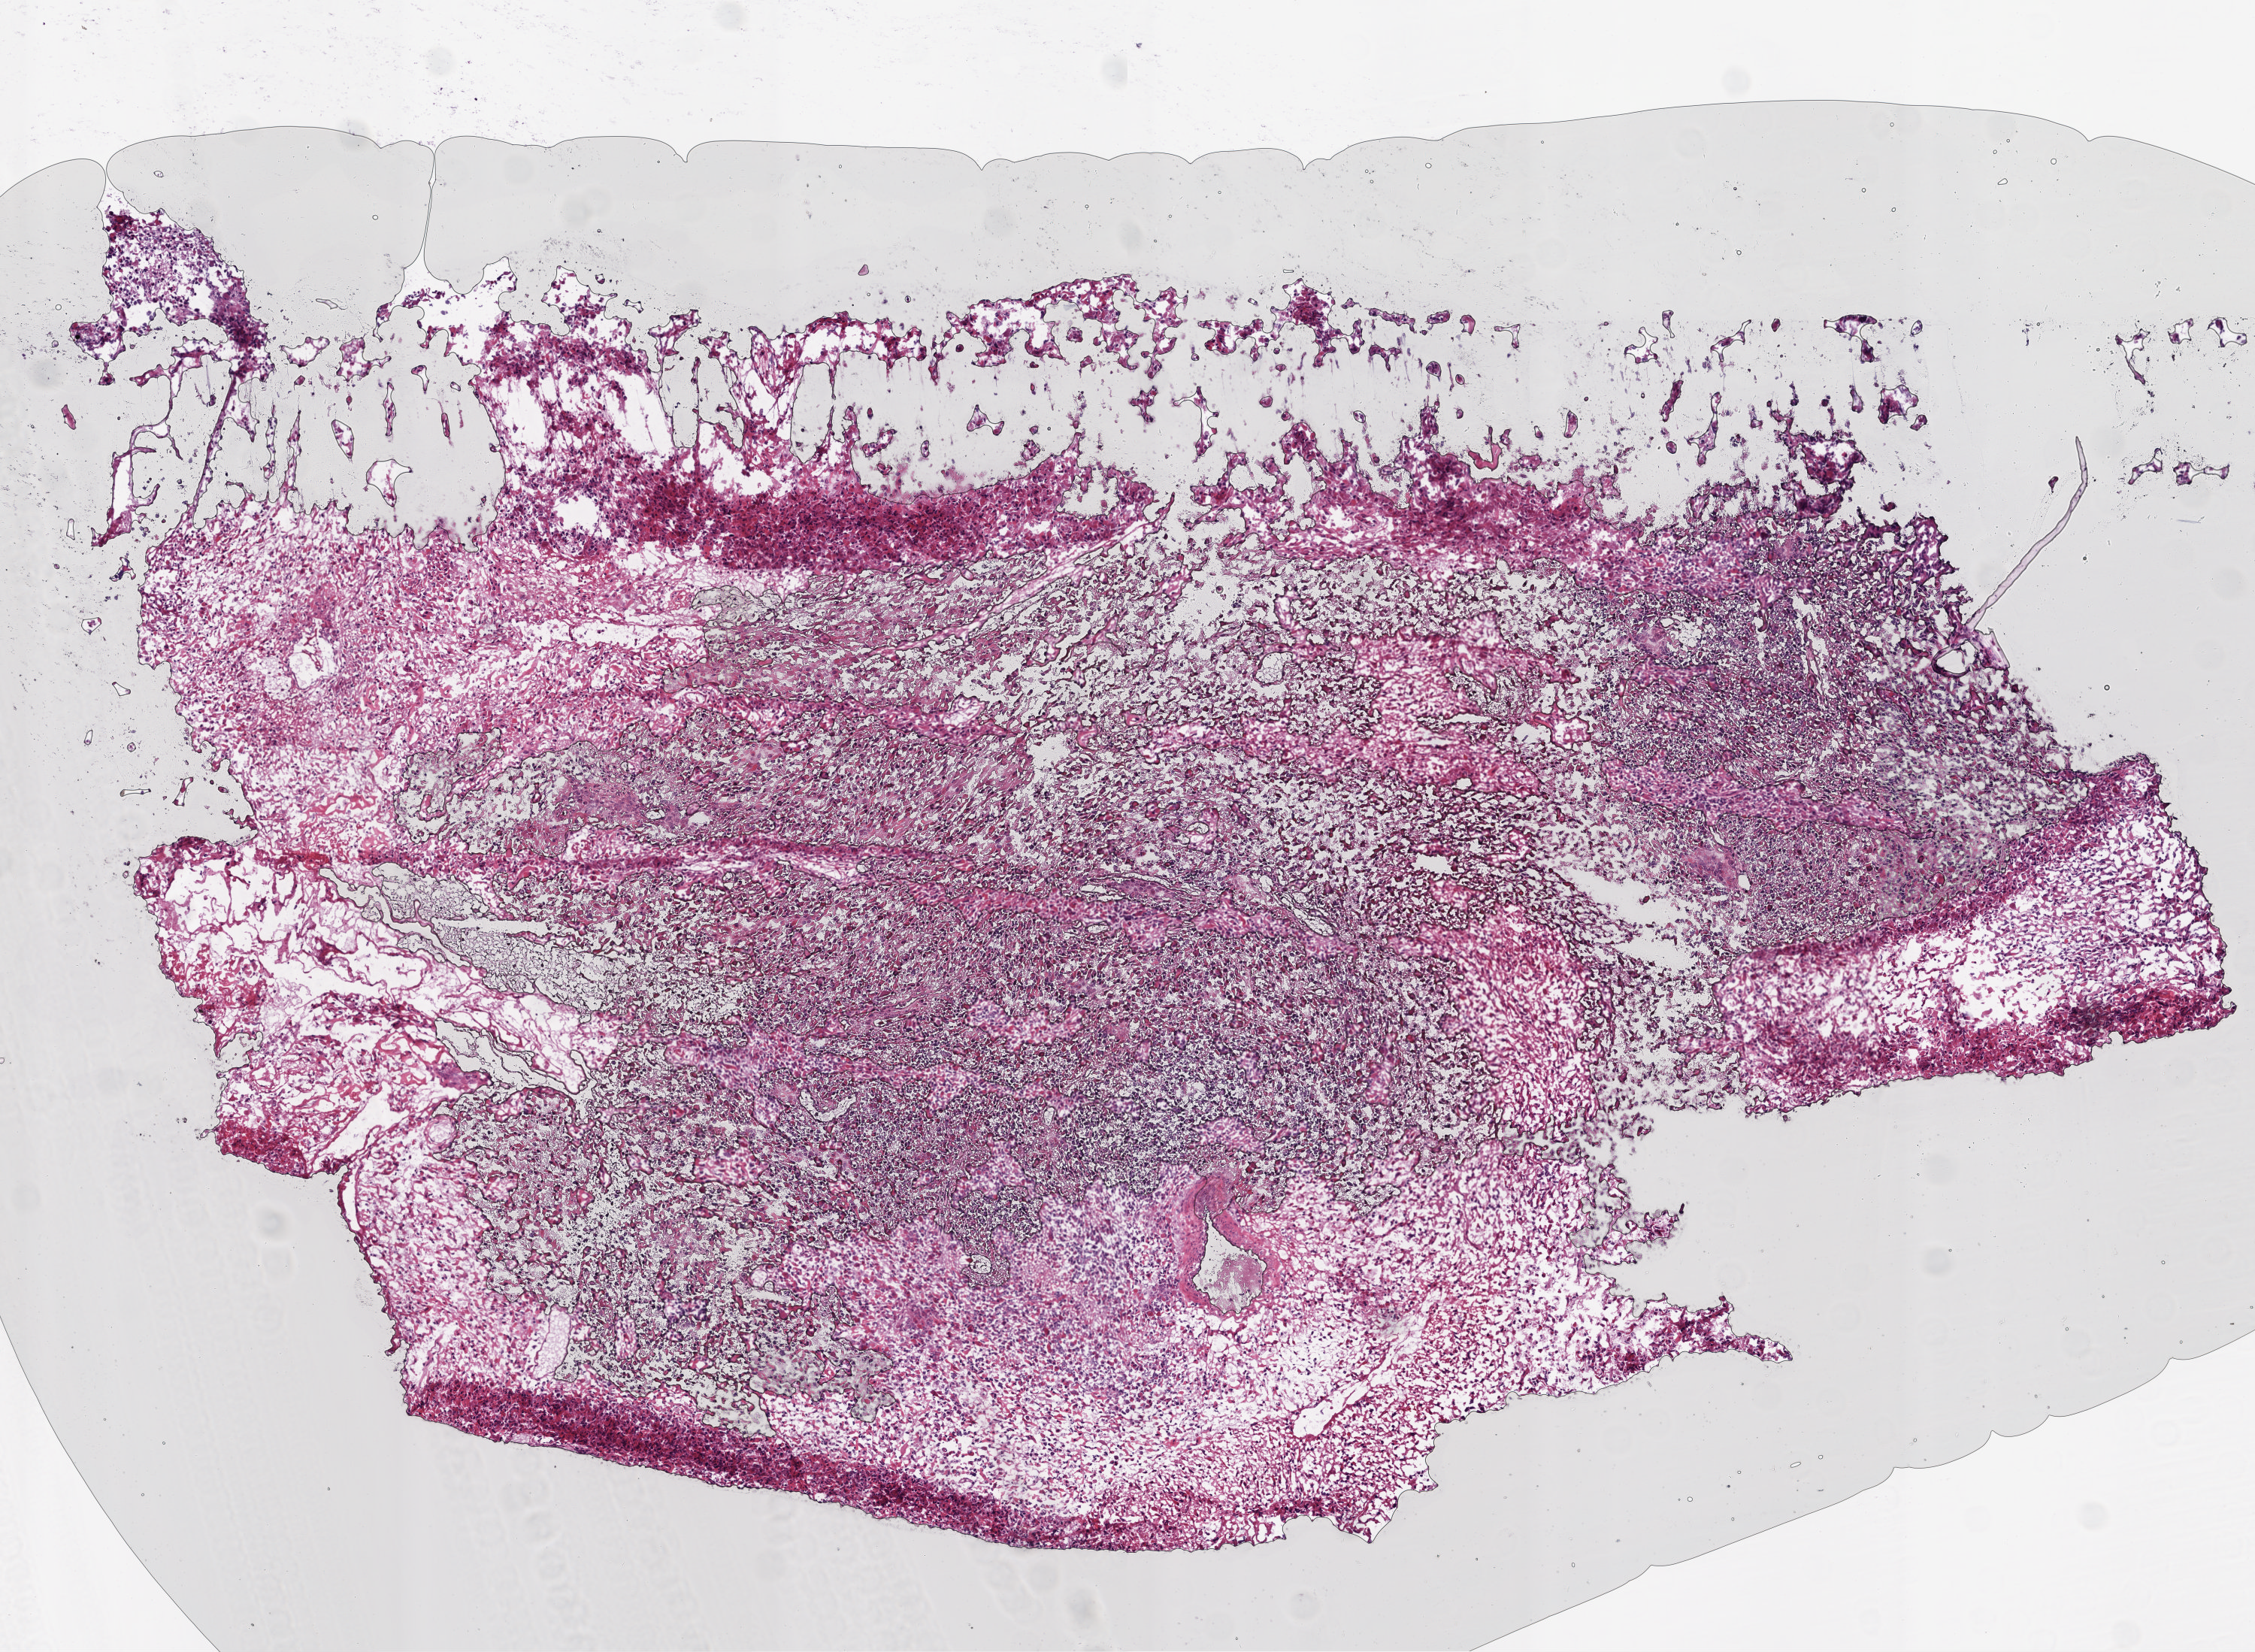
H&E-stained whole-slide image — low-resolution overview of the scanned area, about 6.0 x 4.4 mm, frozen section from the top of the tissue portion, primary tumour sample from the brain. Patient: male, age at initial diagnosis 25 years. Composition of this section per pathologist review: tumour cells 100%, tumour nuclei 85%, normal cells 0%, stromal cells 0%, necrosis 0%.
Histologic diagnosis: Glioblastoma.